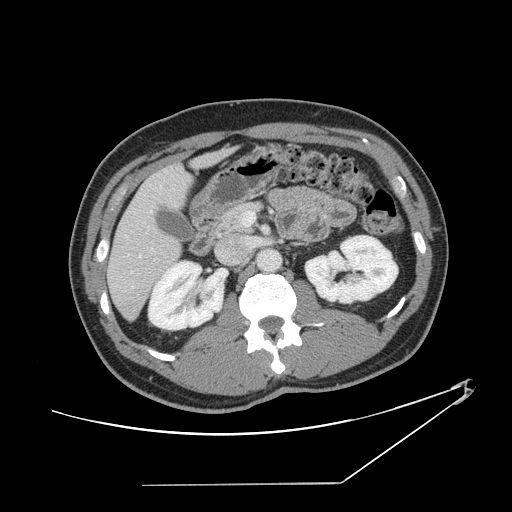
Contrast-enhanced abdominal CT, one axial slice; position 67 of 152 along the scan axis; reconstruction kernel STANDARD; 120 kVp; intravenous contrast given; soft-tissue window (W 400 / L 40 HU); 2.5 mm slice thickness; 512 × 512 image matrix, field of view 432 × 432 mm. Male patient, age 45 years. Case-level facts recorded for this patient, not image findings: diagnosis: colorectal cancer liver metastases, imaged before liver resection; multiple liver metastases: no; largest metastasis: 1 cm; disease in both lobes: no.
Annotated regions visible in this slice (outlined manually by an expert reader):
- hepatic veins: bounding box (x1, y1, x2, y2) in pixels: (125, 187, 161, 258)
- liver: (109, 150, 229, 319)
- planned liver remnant (the part of the liver to remain after resection): (109, 166, 192, 319)
- portal vein (with intrahepatic branches): (242, 211, 255, 226)